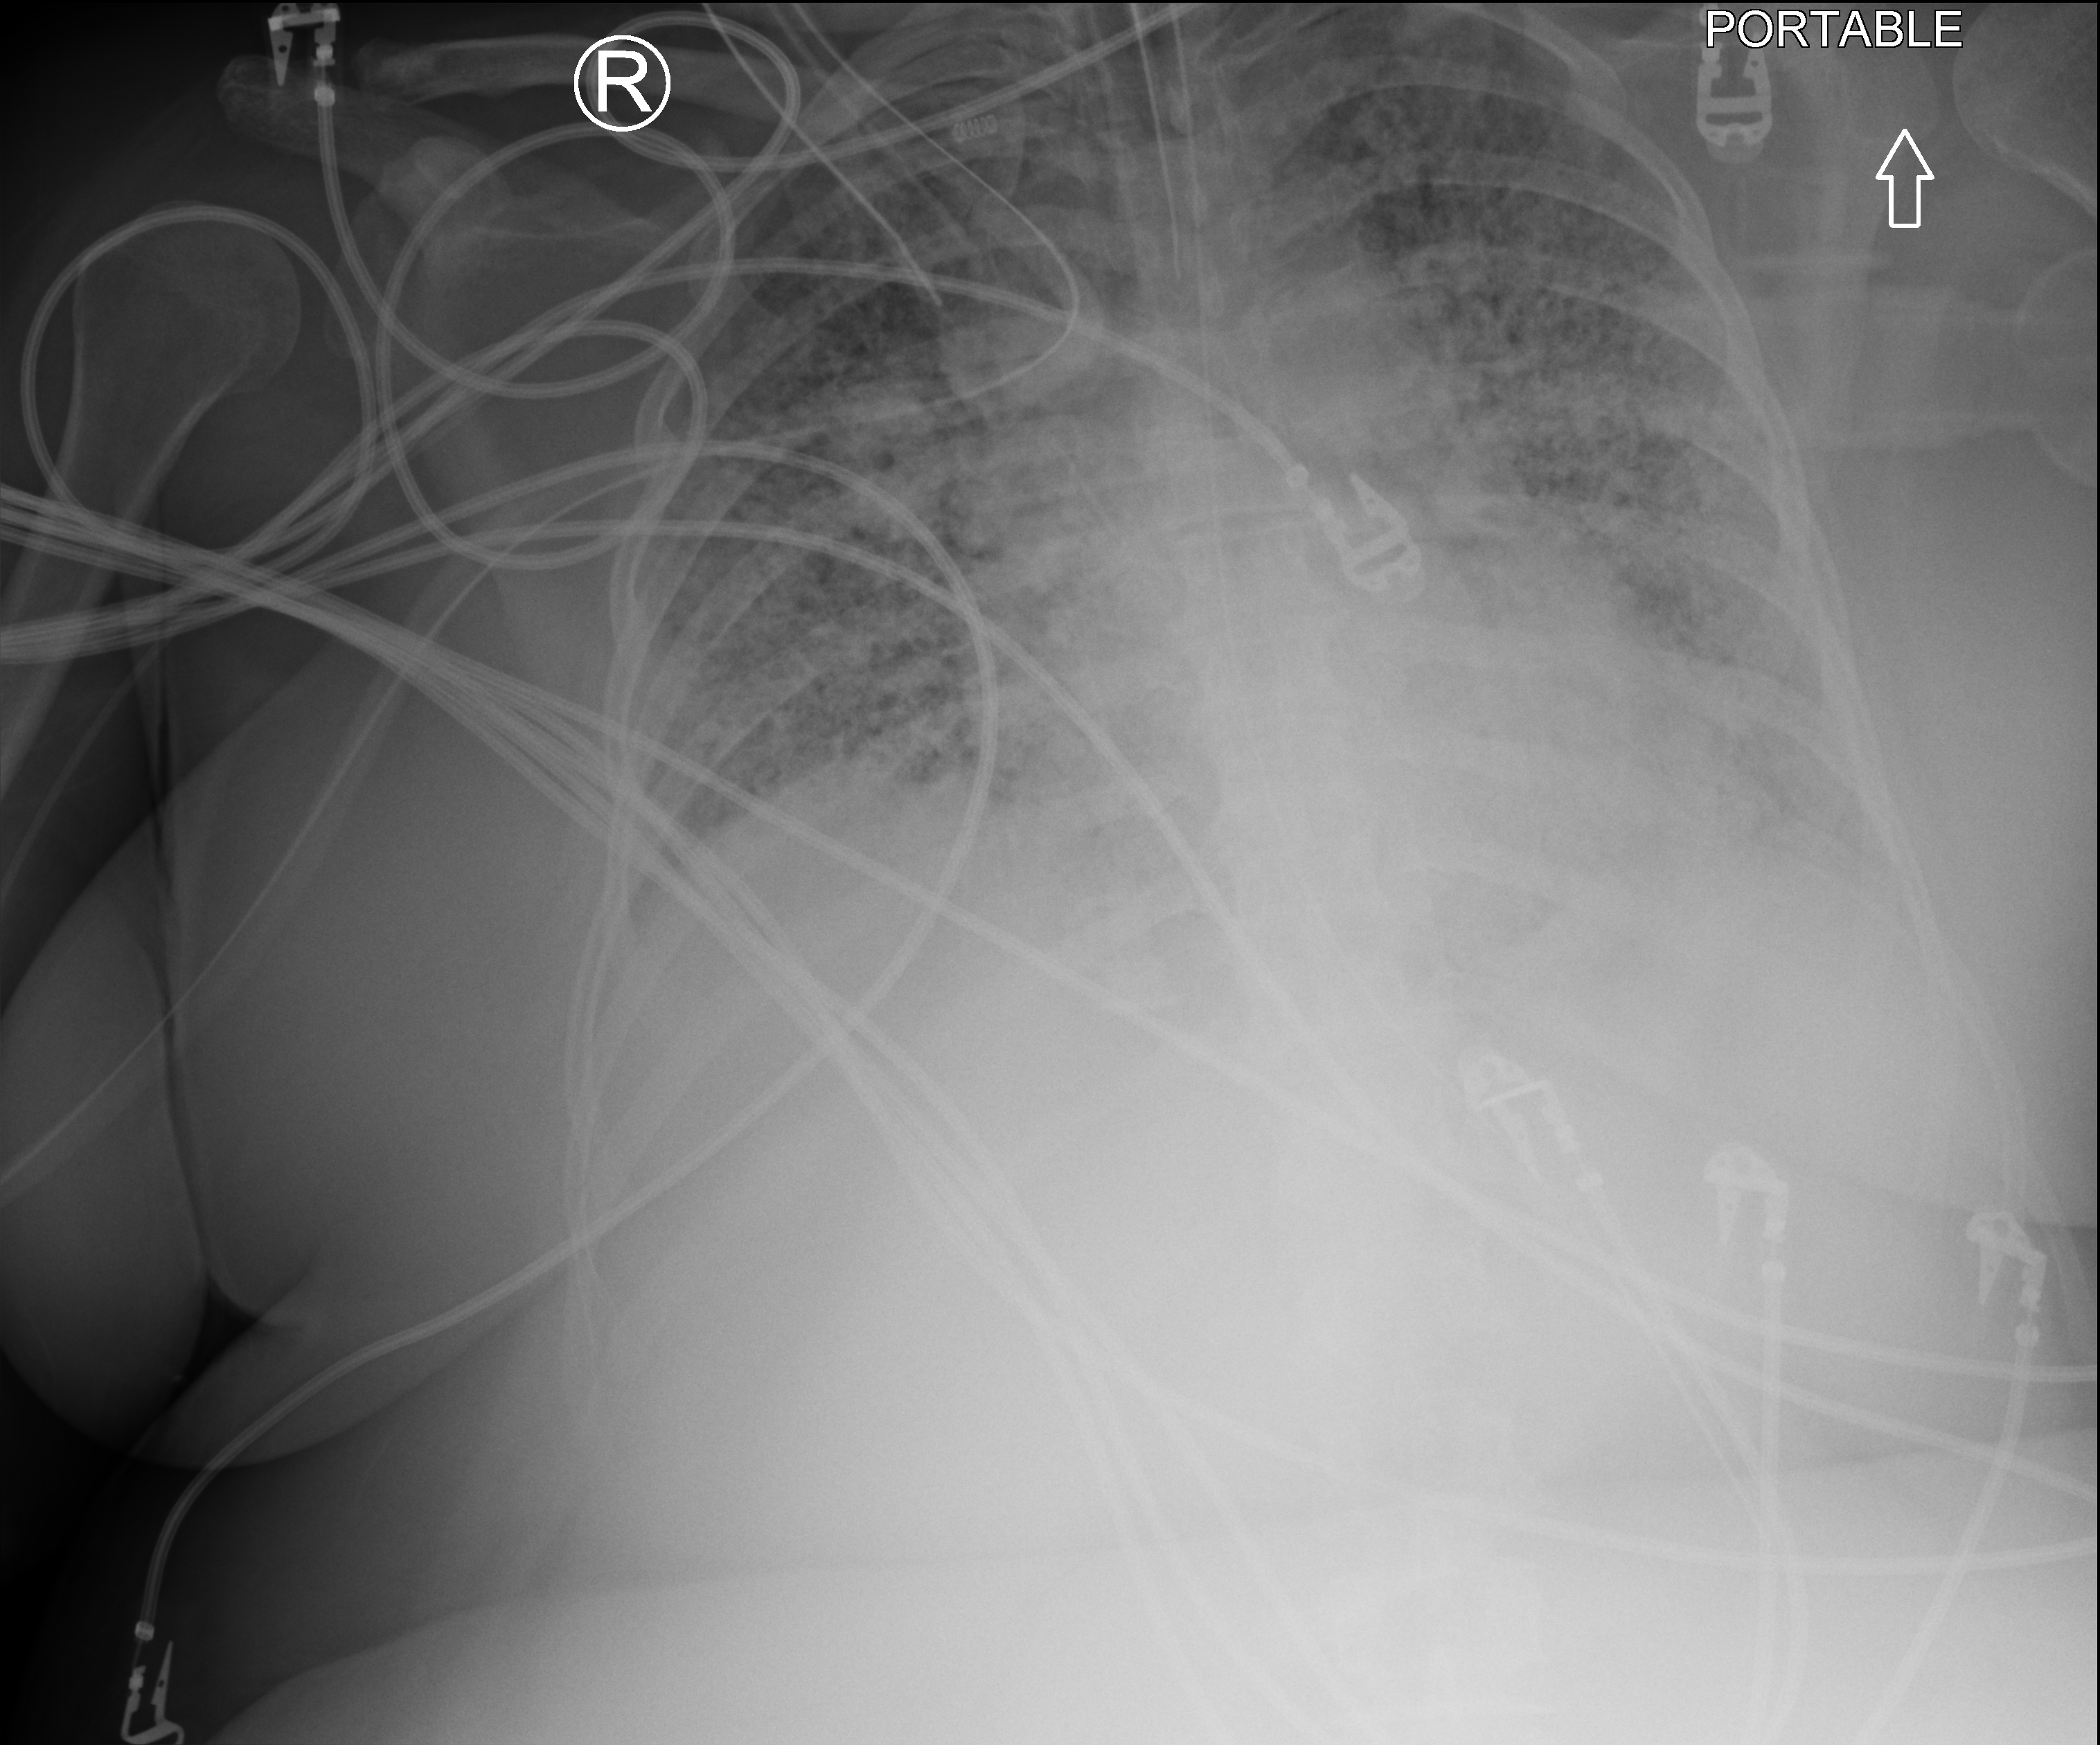
Portable chest radiograph; anteroposterior (AP) projection. Female patient hospitalised with COVID-19, age 18–59 years.
Hospital-stay facts (about this admission, not read from this image; timing relative to this image not recorded):
- hypertension (admission record): yes
- chronic kidney disease (admission record): no
- mechanically ventilated during this hospital stay: yes